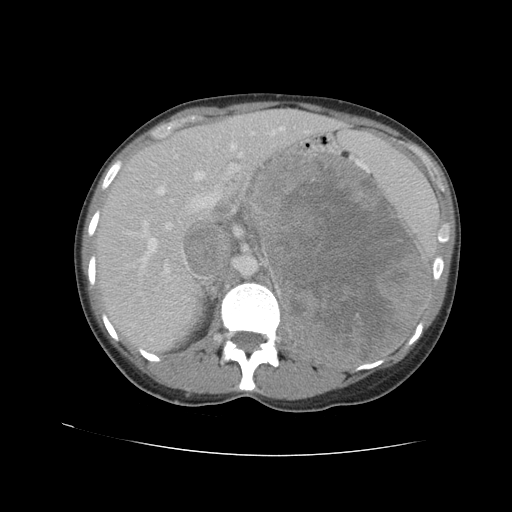
Contrast-enhanced abdominal CT, one axial slice; position 67 of 90 along the scan axis; reconstruction kernel STANDARD; 120 kVp; intravenous contrast given; soft-tissue window (W 400 / L 40 HU); 5 mm slice thickness; 512 × 512 image matrix, field of view 360 × 360 mm. Female patient. From the clinical record (not read from this slice): diagnosis: adrenocortical carcinoma; tumour side: left adrenal; tumour size at pathology: 18 cm; Ki-67 index: 11 %; stage (as recorded): 3.
Outlined on this slice (semi-automatically segmented with operator editing):
- mass: bounding box [x1, y1, x2, y2] px = [252, 155, 431, 363]